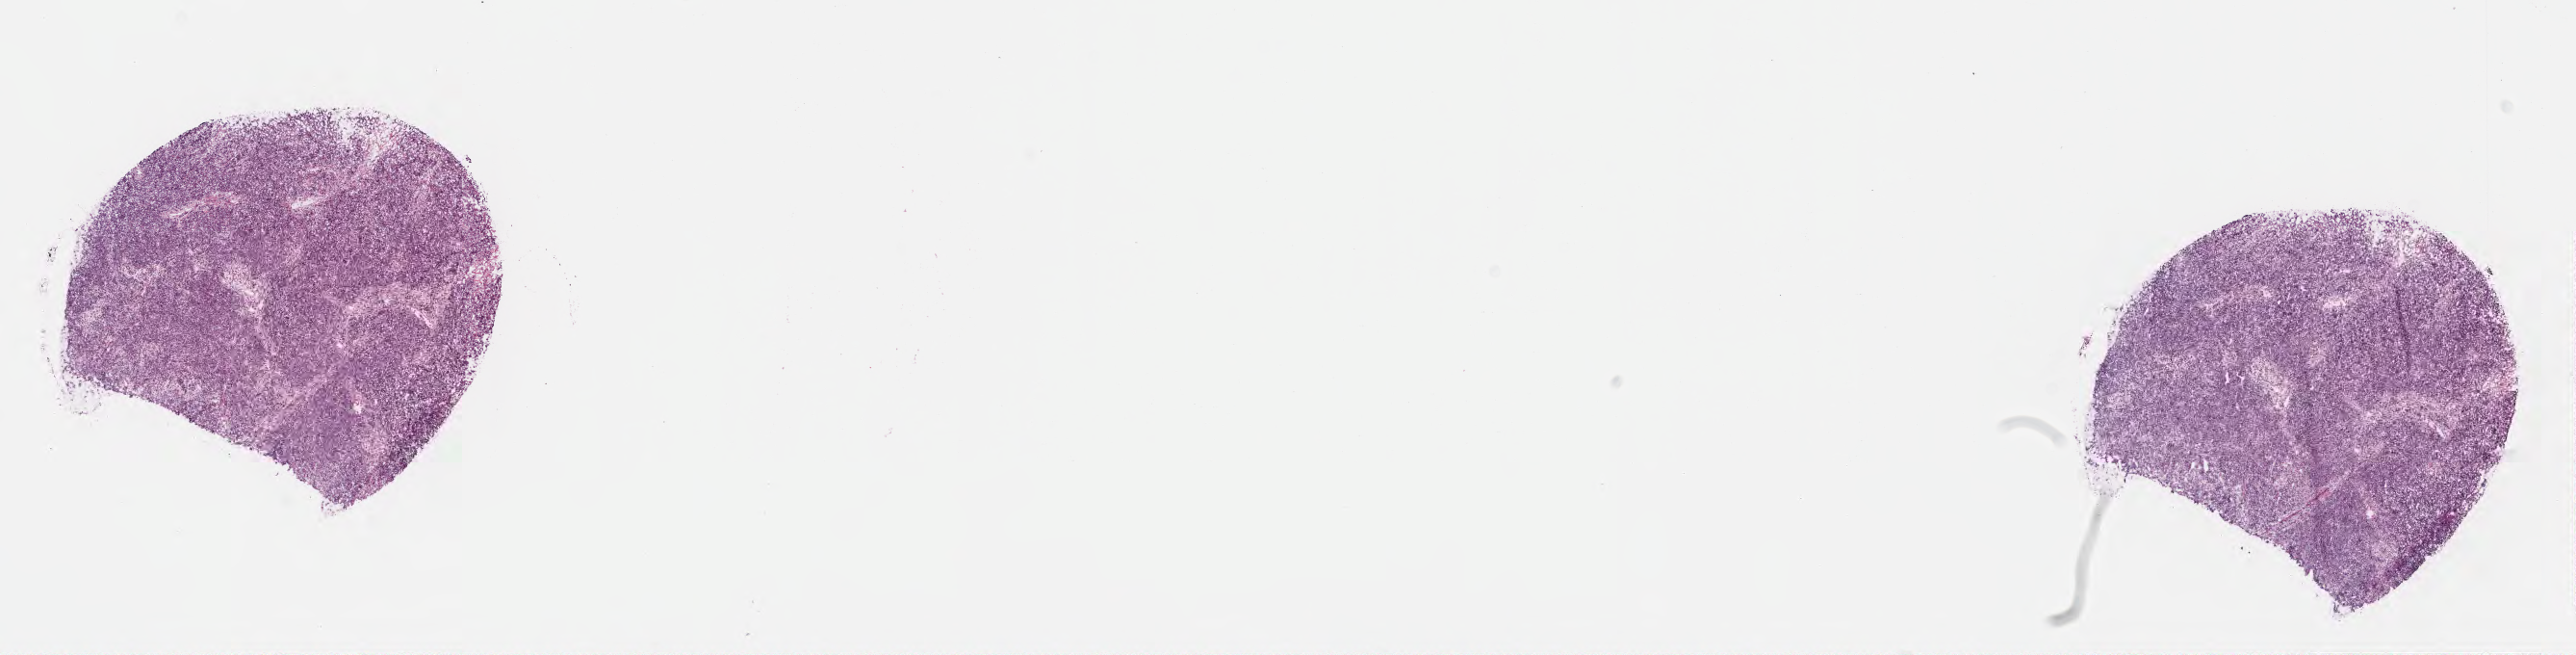
Hematoxylin and eosin (H&E) whole-slide image, a low-resolution overview of the entire scanned area, about 21.6 x 5.5 mm. Frozen section. Metastatic tumor tissue, resected from lymph node. Patient: male, age at initial diagnosis 70 years.
Patient diagnosis (primary): Carcinoma, NOS.